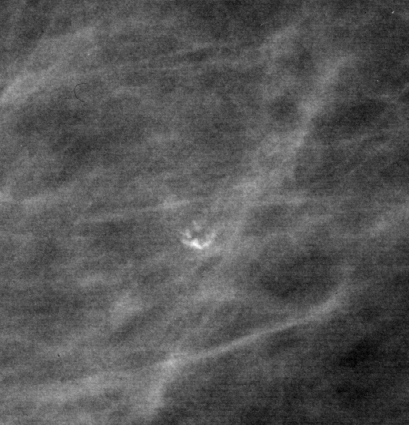
Crop from a digitized film mammogram around one marked abnormality, right breast, MLO view, BI-RADS breast density category 2 (scale 1–4).
Finding: calcifications, morphology amorphous, distribution clustered; BI-RADS assessment category 4; pathology result (as recorded, not read from the image): benign.